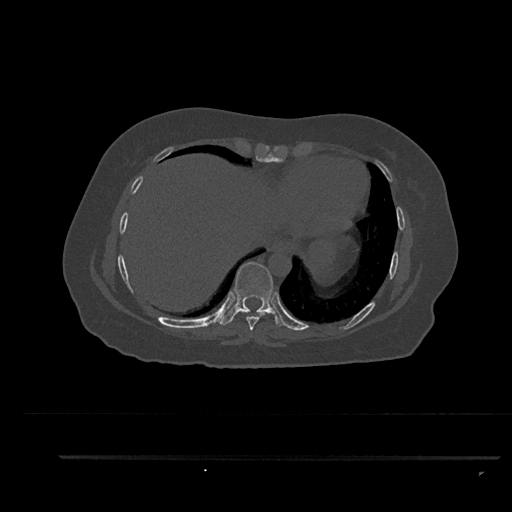
CT including the spine, one axial slice; 120 kVp; bone window (W 1800 / L 400 HU); 0.5 mm slice thickness; 512 × 512 image matrix, field of view 408 × 408 mm. Female patient, age 44 years. From the clinical record (not read from this slice): primary cancer: renal; vertebrae with lytic lesions (as recorded): L1.
Outlined on this slice (semi-automatically segmented with operator editing):
- T8 vertebra: bounding box [x1, y1, x2, y2] px = [240, 310, 266, 331]
- T9 vertebra: [219, 262, 284, 327]